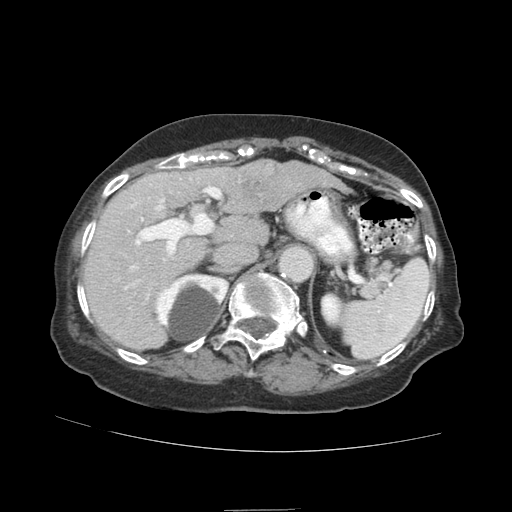
Contrast-enhanced abdominal CT (liver protocol), one axial slice; position 57 of 89 along the scan axis; reconstruction kernel STANDARD; 140 kVp; soft-tissue window (W 400 / L 40 HU); 512 × 512 image matrix, field of view 360 × 360 mm. Case-level facts recorded for this patient, not image findings: diagnosis: hepatocellular carcinoma (patient treated with transarterial chemoembolisation; whether this scan precedes or follows treatment is not stated here); TNM stage (as recorded): Stage-II; Child-Pugh class: A.
Structures marked on this image (semi-automatically segmented with operator editing):
- liver parenchyma outside the tumour (the mass and vessels are separate outlines, so this box may not span the whole liver): bounding box [x1, y1, x2, y2] px = [84, 160, 330, 350]
- mass: [228, 159, 292, 213]
- liver vessels: [92, 178, 222, 324]